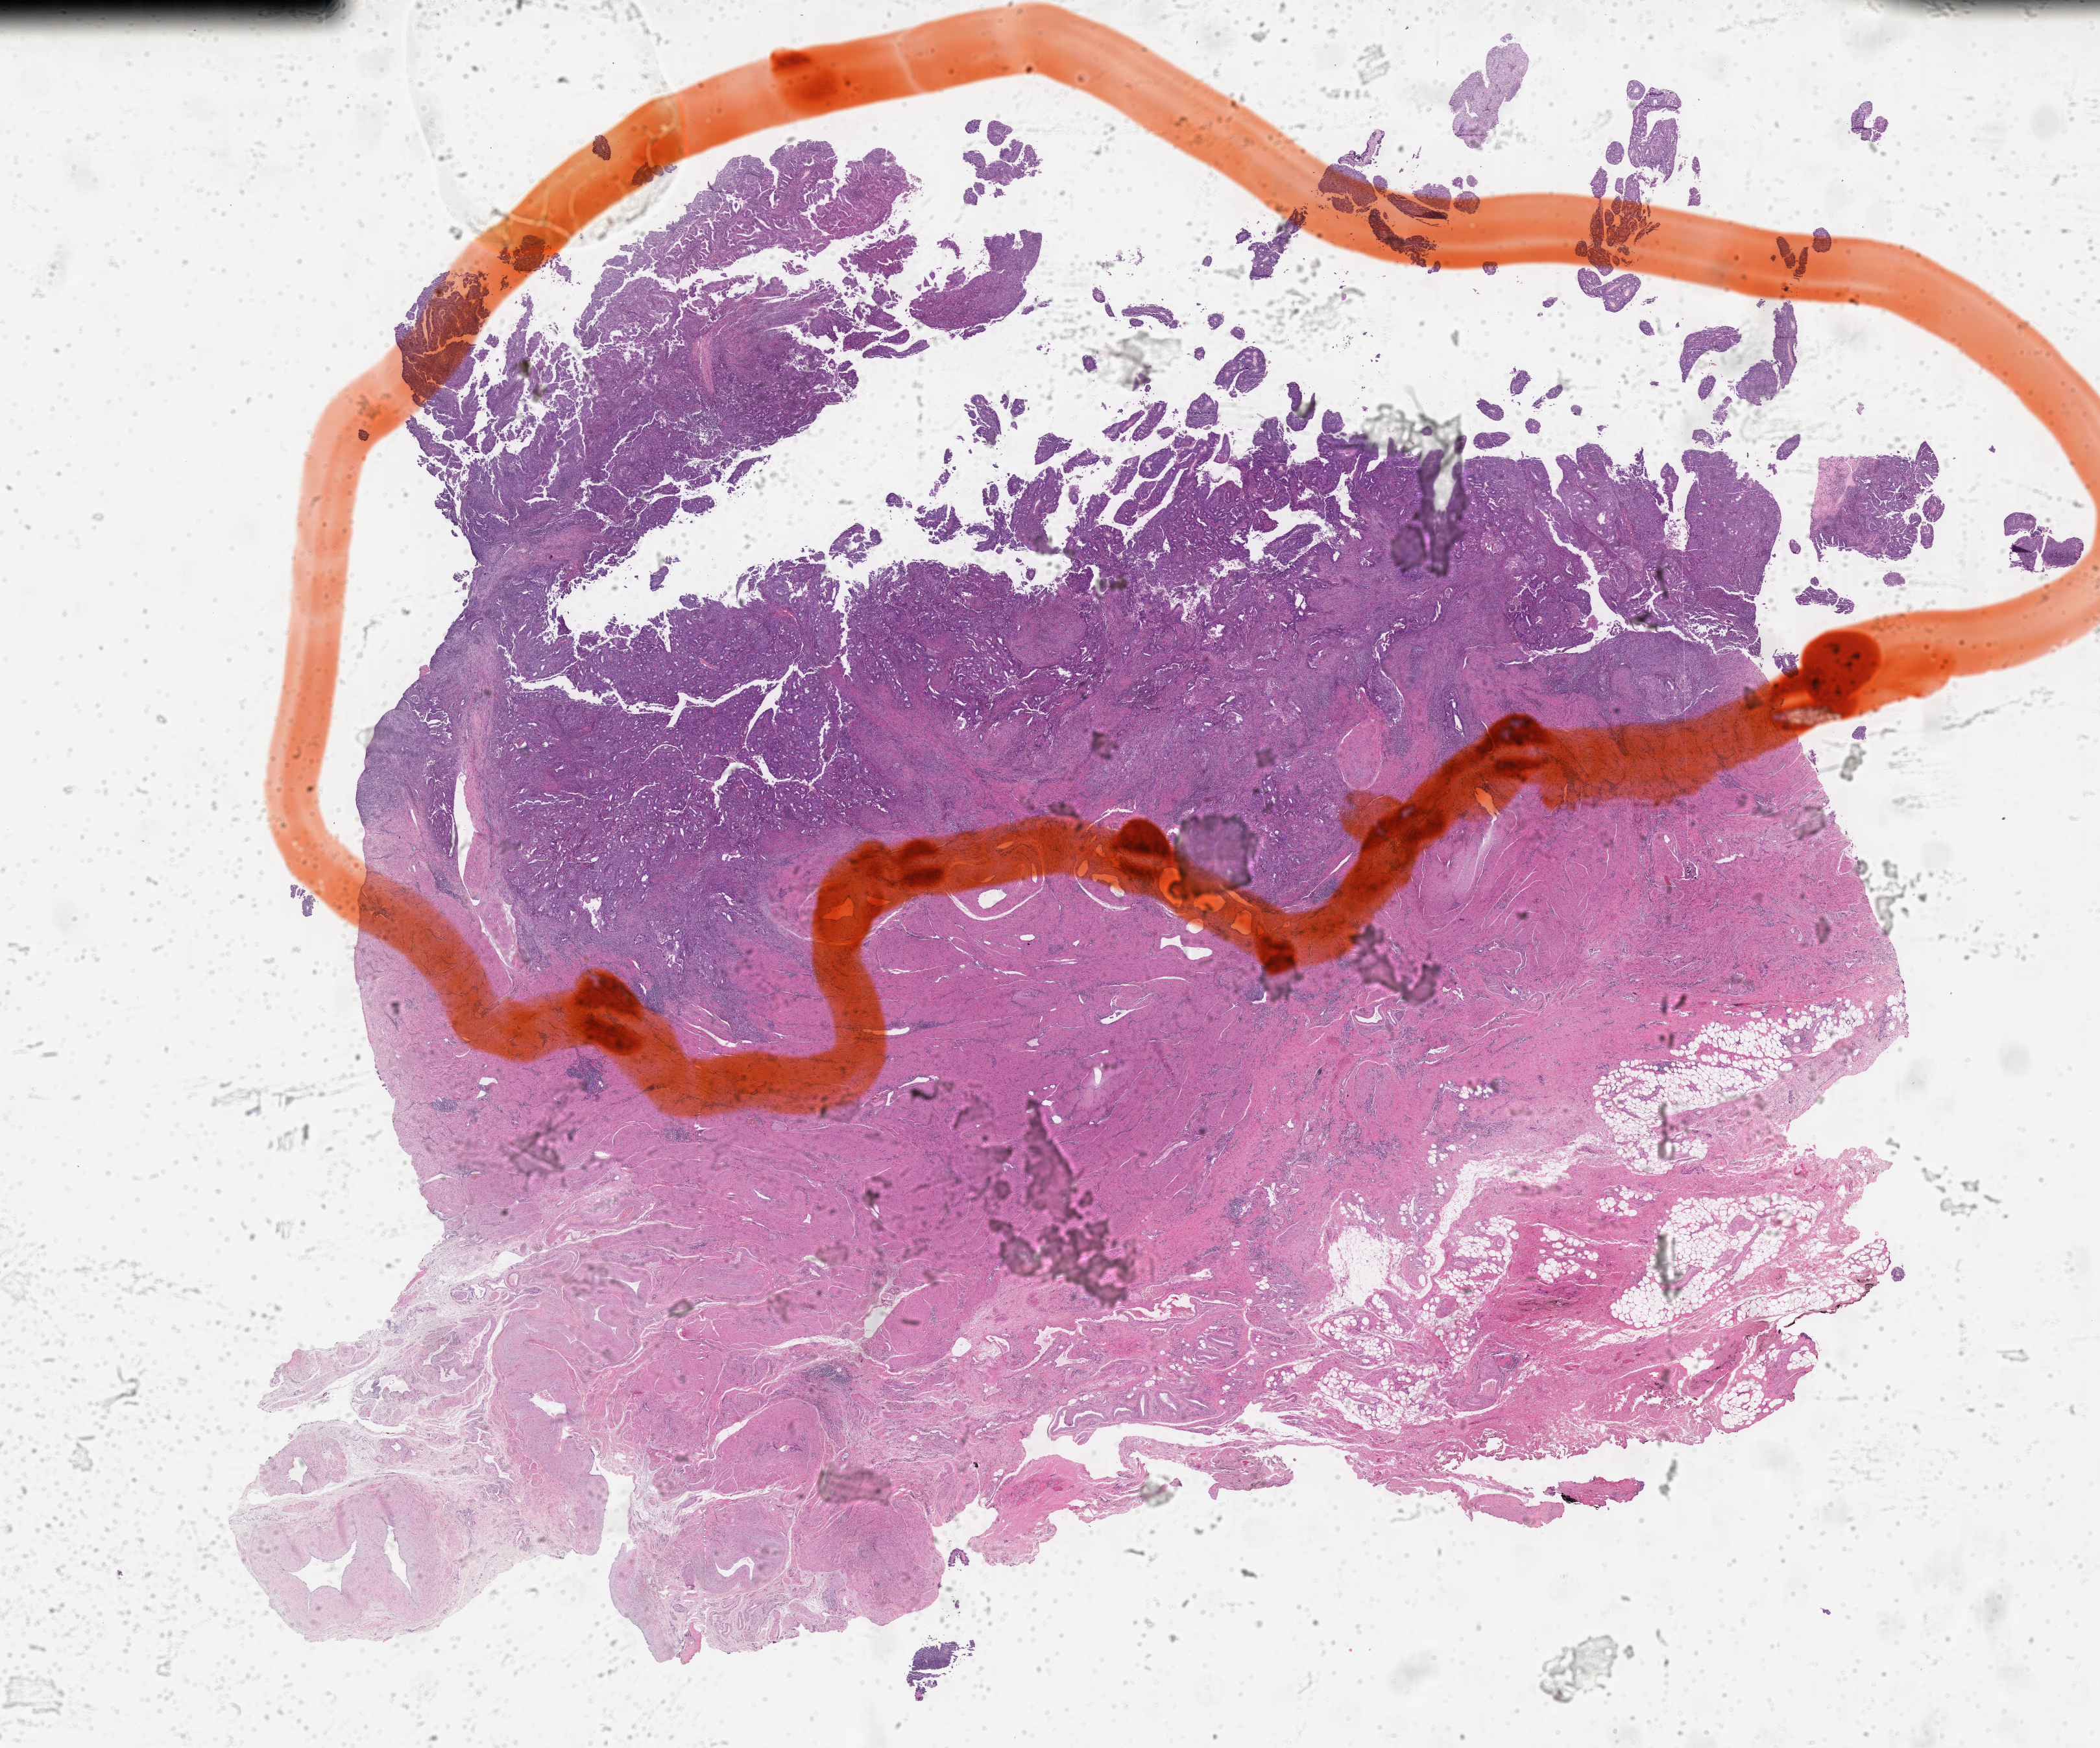
Digitized haematoxylin and eosin-stained section, low-resolution overview of the scanned area, about 26.1 x 21.7 mm. Formalin-fixed paraffin-embedded section. Primary tumor. Anatomic site: endometrium. Female, age 34 years at initial diagnosis. Tumor grade: G2 (moderately differentiated). Pathologist review of this section (percent, as recorded): tumor cells 40%, tumor nuclei 40%, stromal cells 0%, necrosis 0%, normal cells 60%. Infiltration values recorded for this section: lymphocyte infiltration 0%, monocyte infiltration 0%, neutrophil infiltration 0%.
• histologic diagnosis: Endometrioid adenocarcinoma, NOS
• FIGO stage: Stage IIIC2